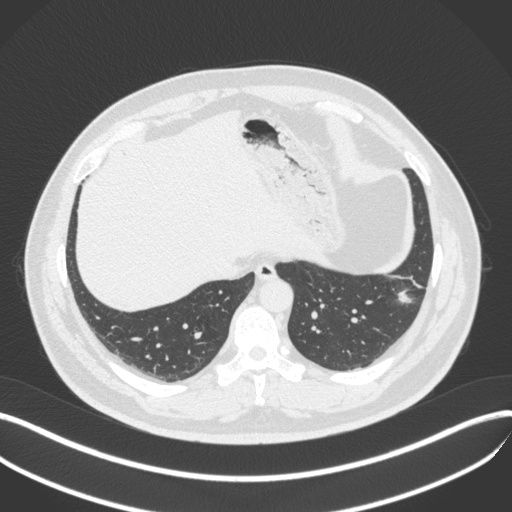
Chest CT, one axial slice; slice 107 of 420 in the series (ordered by position); lung window (W 1500 / L -600 HU); 1 mm slice thickness; 512 × 512 image matrix, field of view 400 × 400 mm. Male patient, age 39 years. Case-level facts recorded for this patient, not image findings: clinical TNM (as recorded): T2a N0 M0.
Outlined on this slice (bounding box drawn by a radiologist):
- lung tumour (recorded histology: adenocarcinoma): bounding box (x1, y1, x2, y2) in pixels: (391, 276, 417, 307)